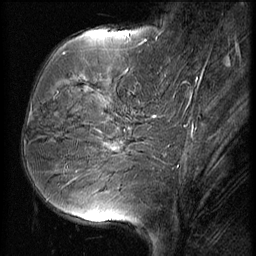
Breast MRI (dynamic contrast-enhanced), one sagittal slice; position 18 of 56 along the scan axis; 3 images stored at this slice position (order not interpretable as contrast timing); 1.5 T; TE 4.2 ms, TR 9 ms; 2.5 mm slice thickness; 256 × 256 image matrix, field of view 180 × 180 mm. Female patient, age 51 years. From the clinical record (not read from this slice): setting: breast cancer imaged before/during neoadjuvant chemotherapy; receptor status: HR-positive, HER2-negative.
Outlined on this slice (semi-automatic segmentation, software-assisted and operator-edited):
- analysis volume of interest (the breast-tissue region the enhancement analysis was run in; not a lesion): bounding box <23,56,156,165> (left, top, right, bottom; pixels)
- tumour enhancement mask (voxels above the 140 % enhancement threshold inside the analysis volume of interest): <112,144,115,151>